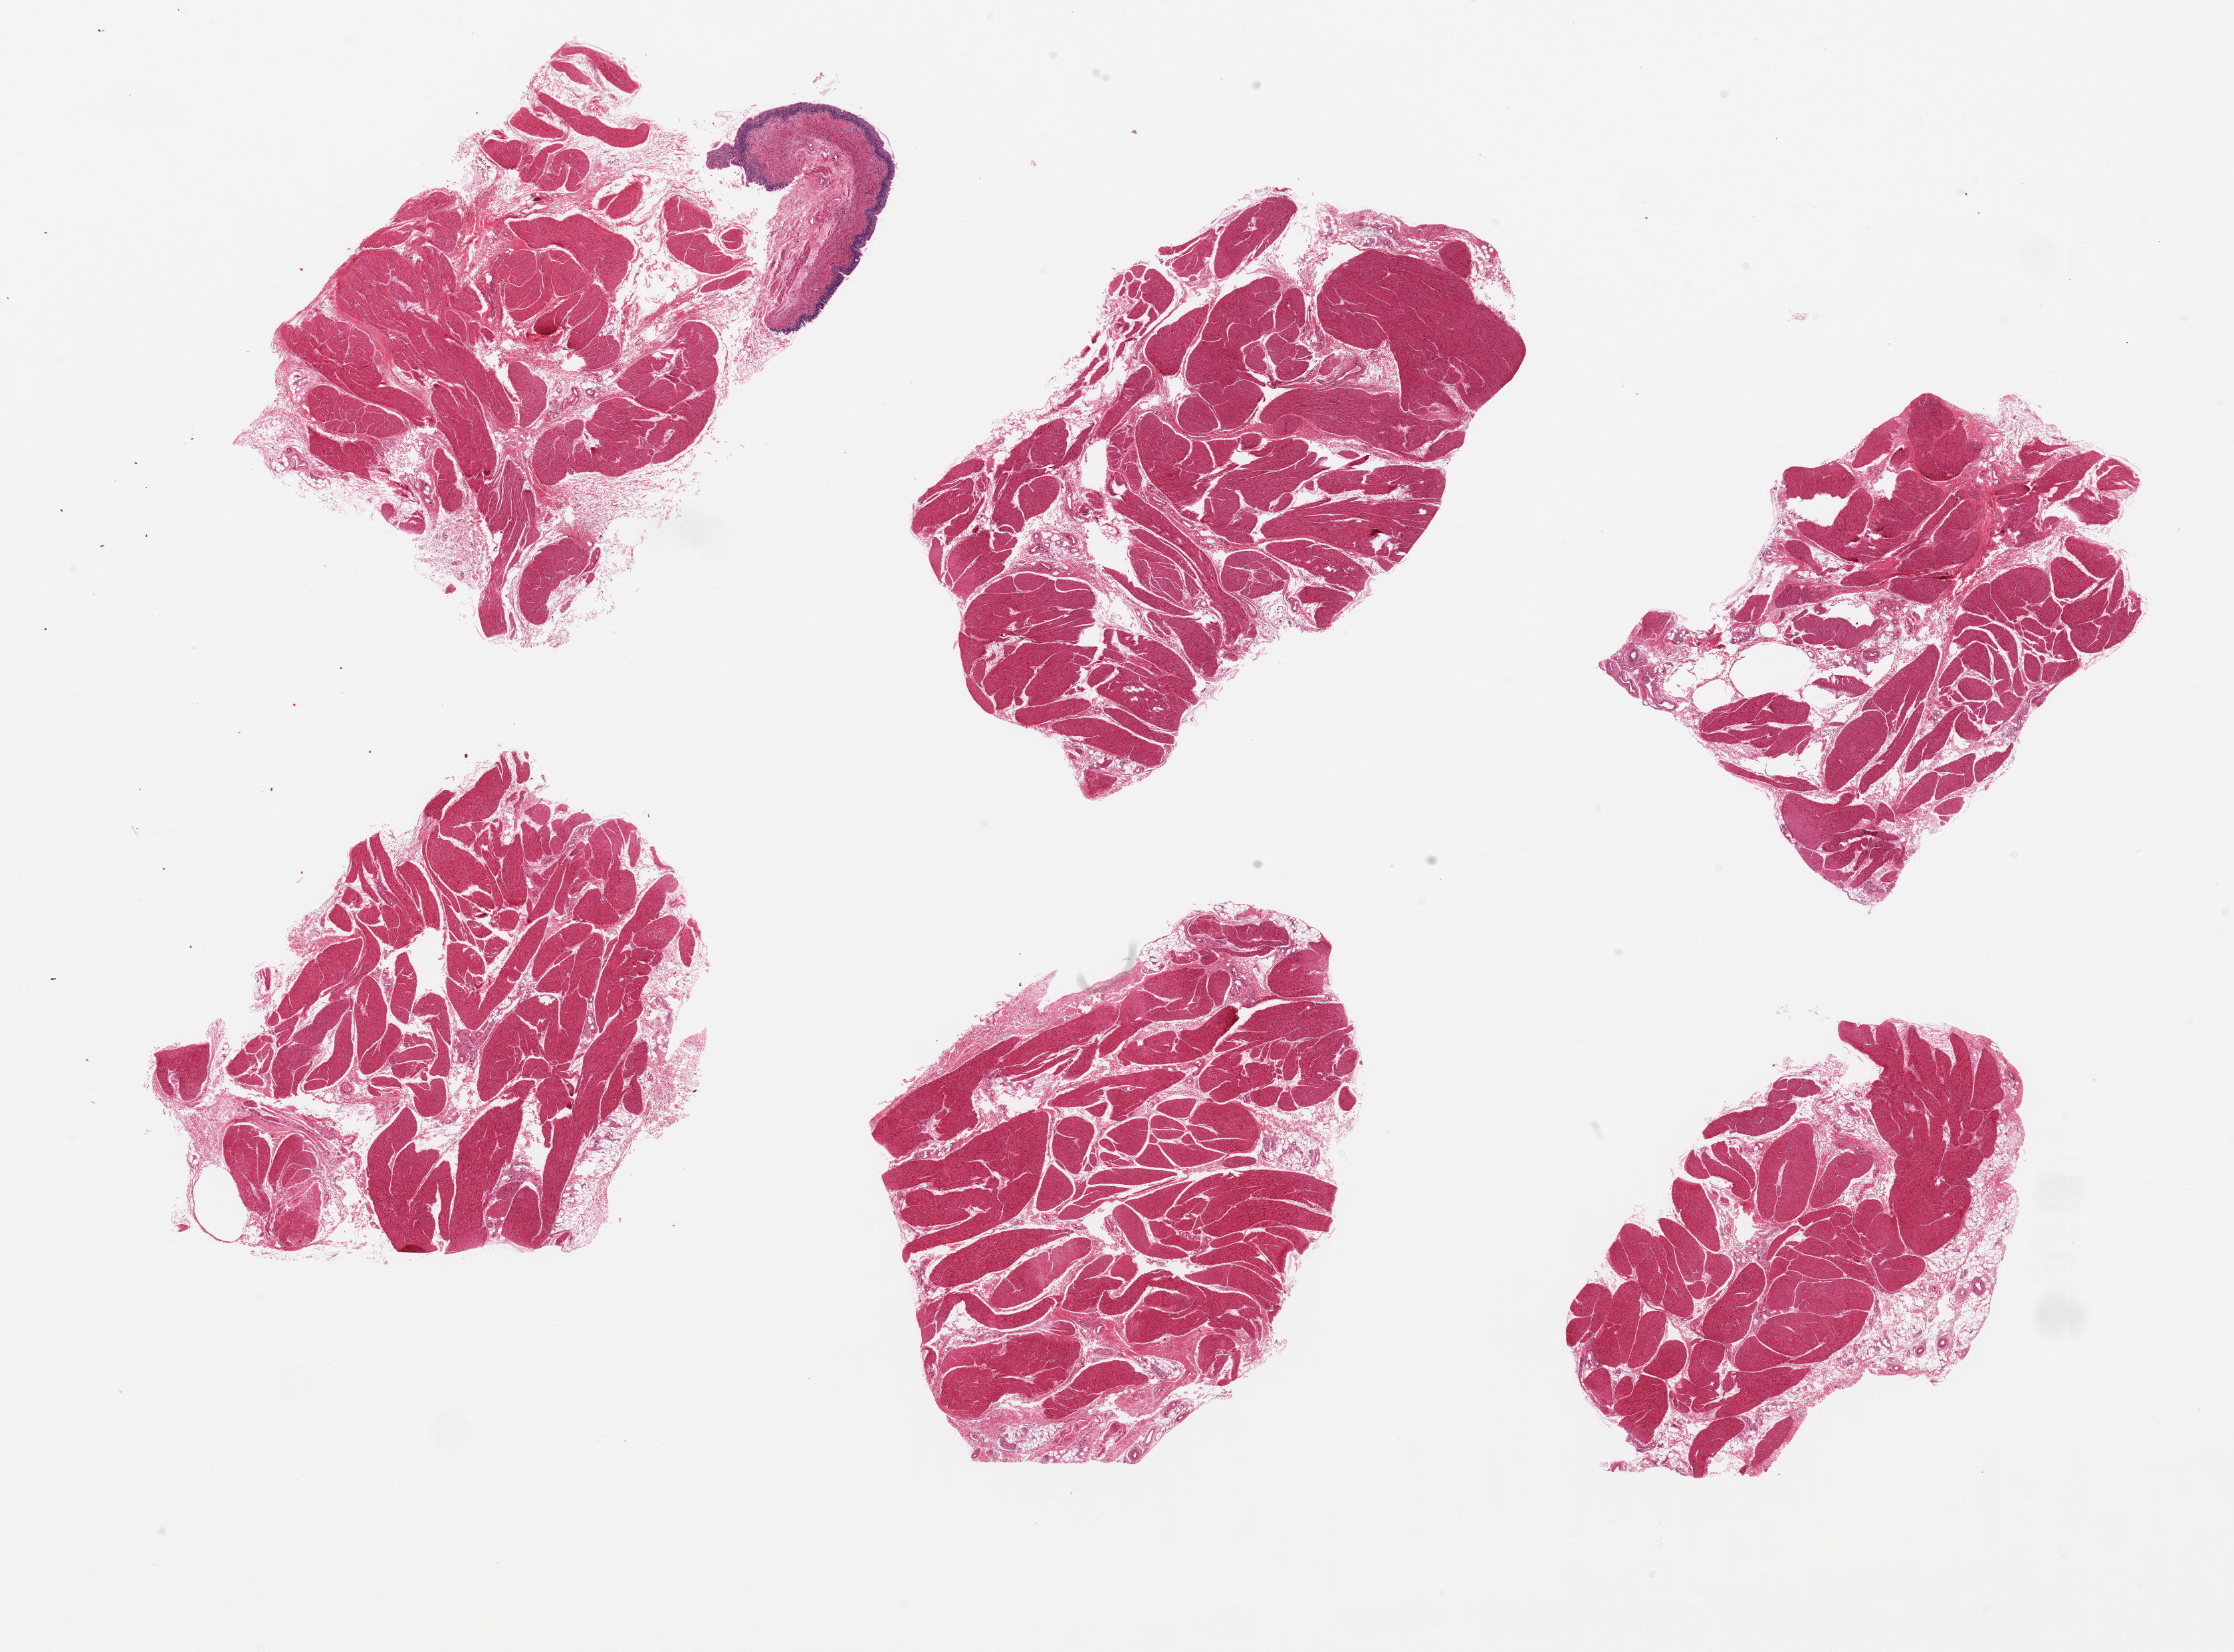
Haematoxylin and eosin whole-slide image, brightfield — low-resolution overview of the scanned area, about 26.6 x 19.7 mm; PAXgene-fixed paraffin-embedded (PFPE) section; target tissue: urinary bladder; tissue donor sample. Donor: female.
- reviewer comment on this tissue sample: 6 pieces up to 8x5 mm; only one piece has mucosa